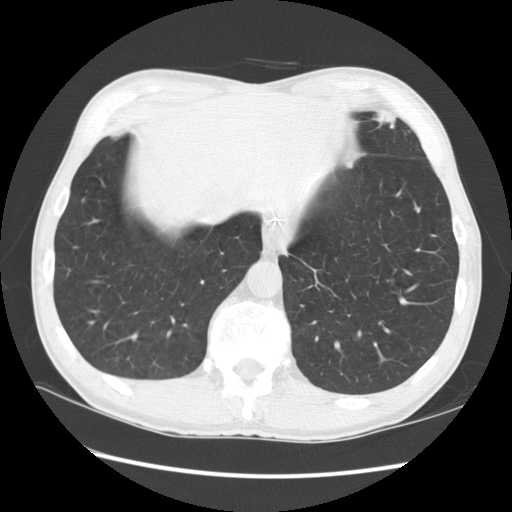
Low-dose screening chest CT, one axial slice; slice 28 of 141 in the series (ordered by position); reconstruction kernel STANDARD; lung window (W 1500 / L -600 HU); 2.5 mm slice thickness; 512 × 512 image matrix, field of view 360 × 360 mm.
Outlined on this slice (expert manual segmentation):
- lesion 1 (tumor, lower lobe of left lung): bounding box (x1, y1, x2, y2) in pixels: (372, 111, 396, 129)